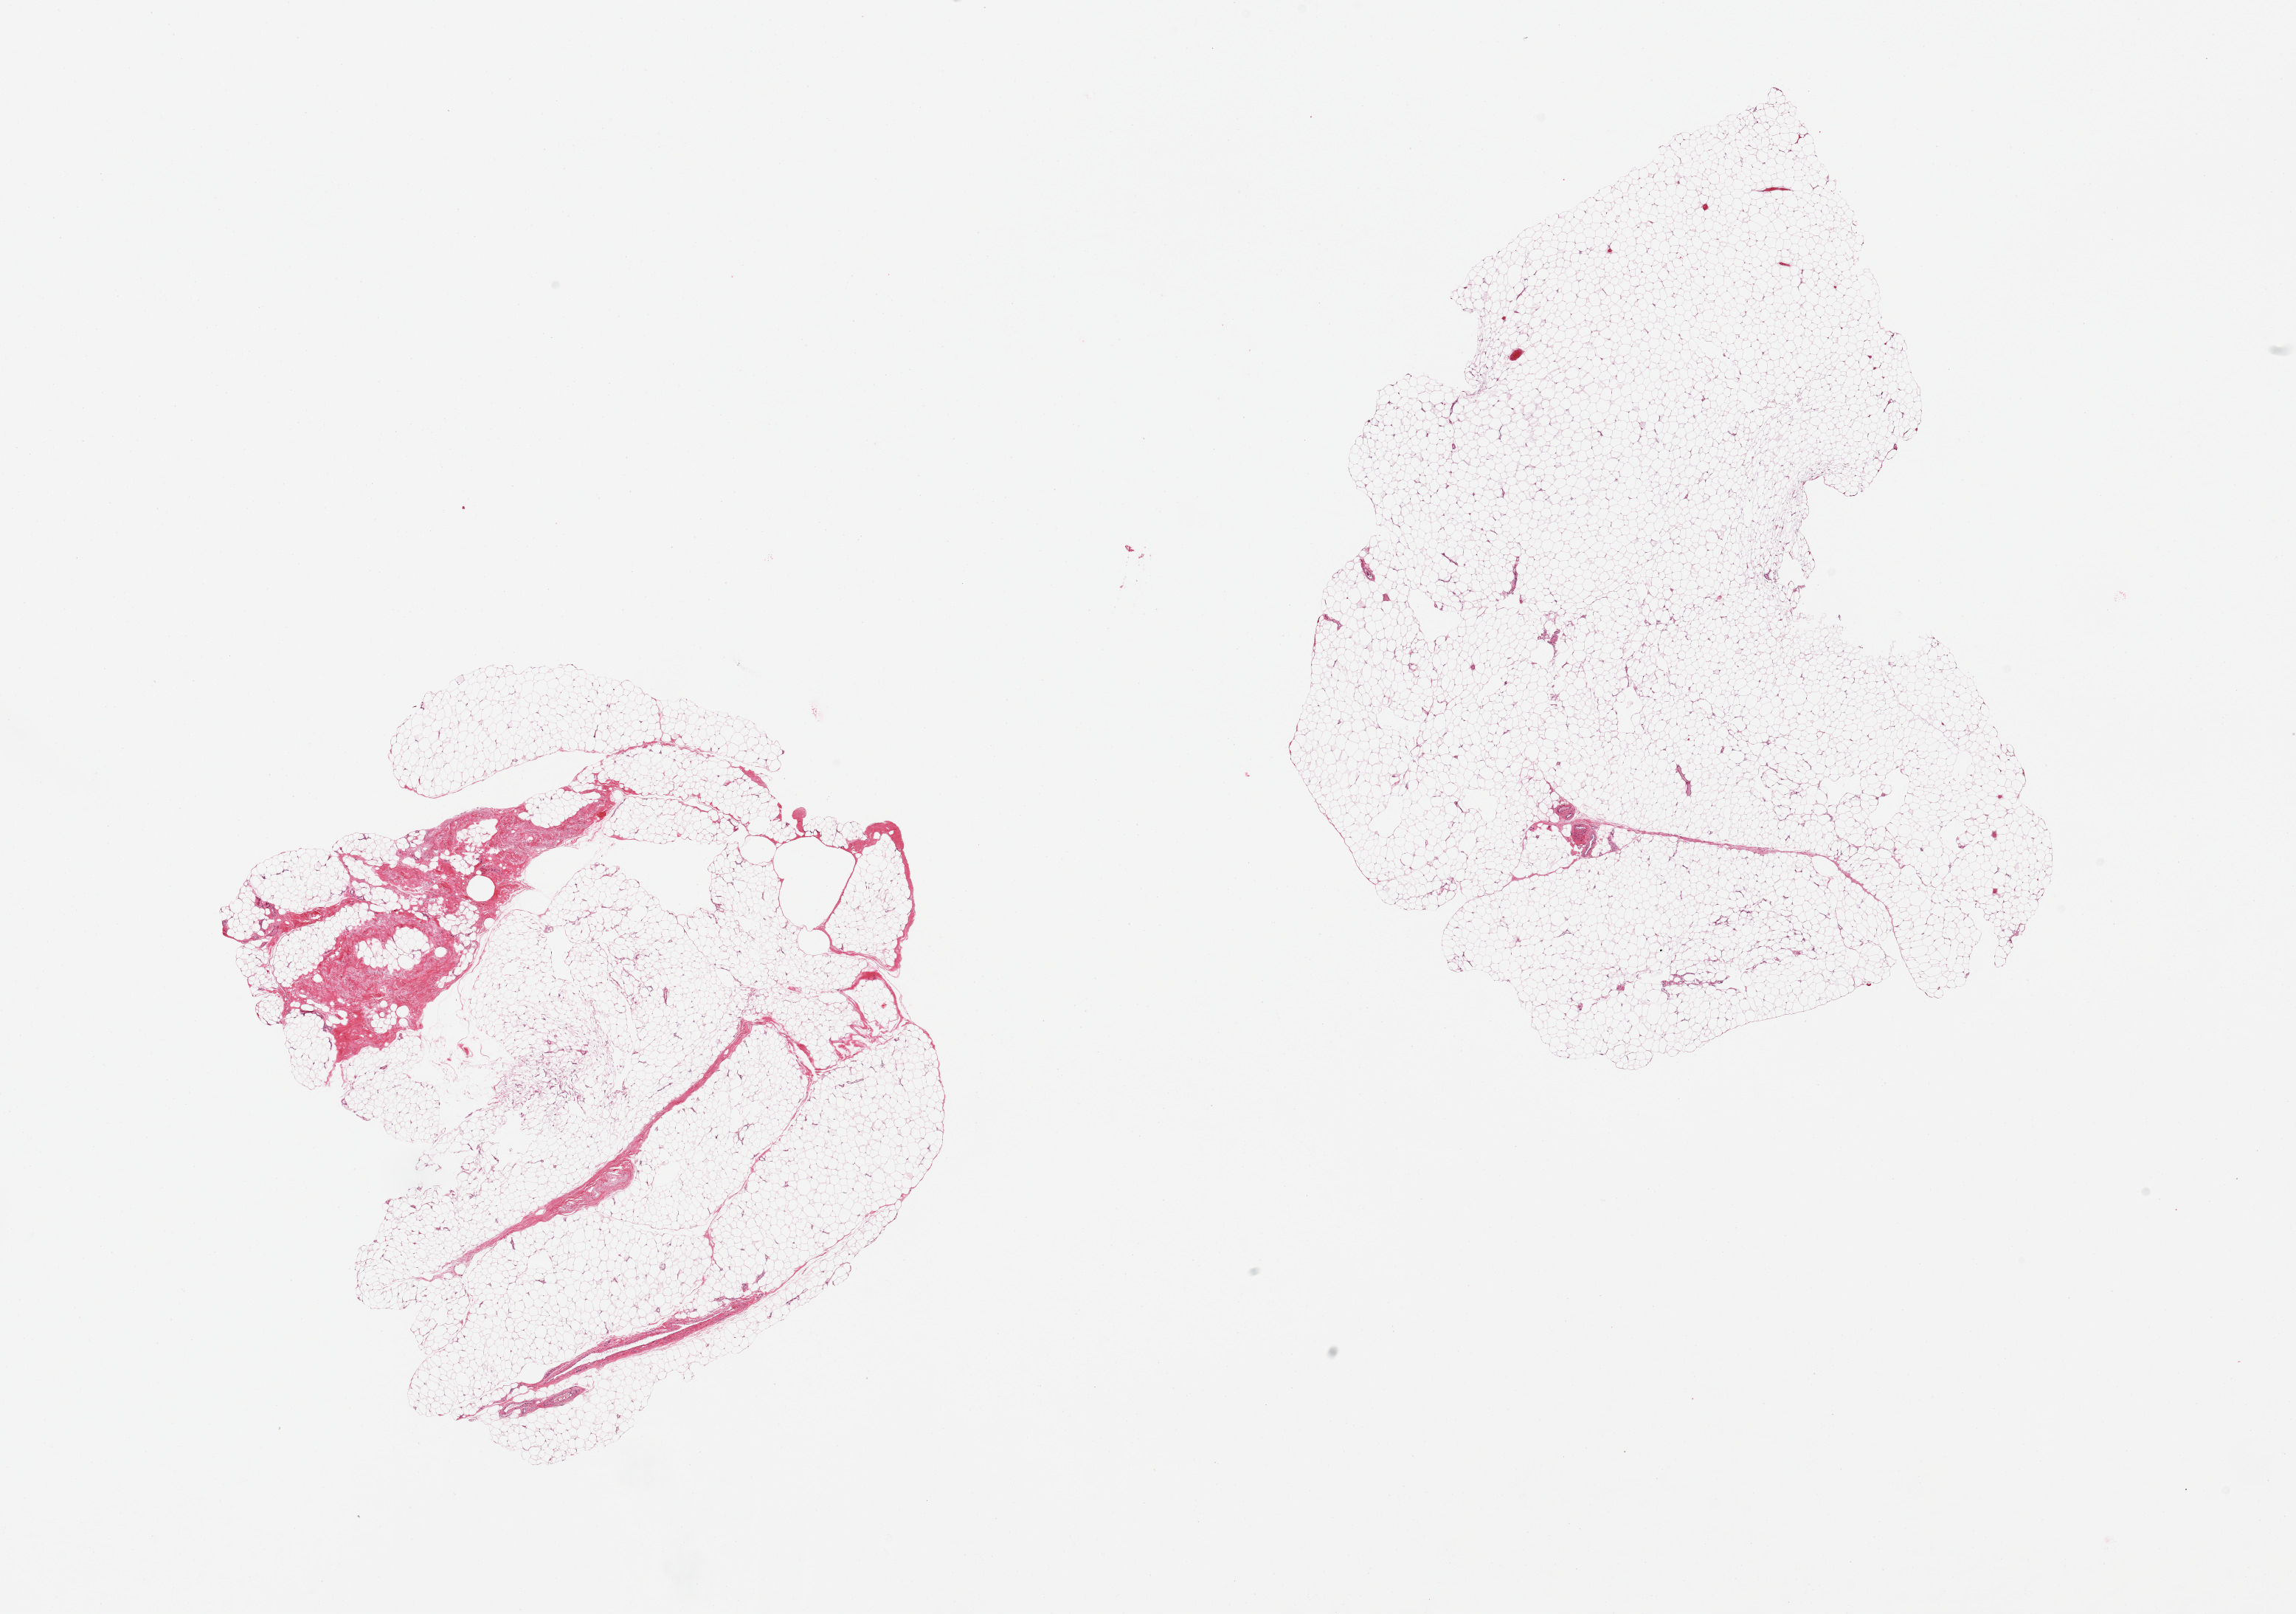
Whole-slide image, hematoxylin and eosin (H&E) stain, whole scanned area (about 24.6 x 17.3 mm) shown as a low-resolution overview, PAXgene-fixed paraffin-embedded (PFPE) section, sampled site (target tissue): adipose tissue, donor tissue sample. Donor sex: male.
Pathologist's review note for this sample: 2 pieces.